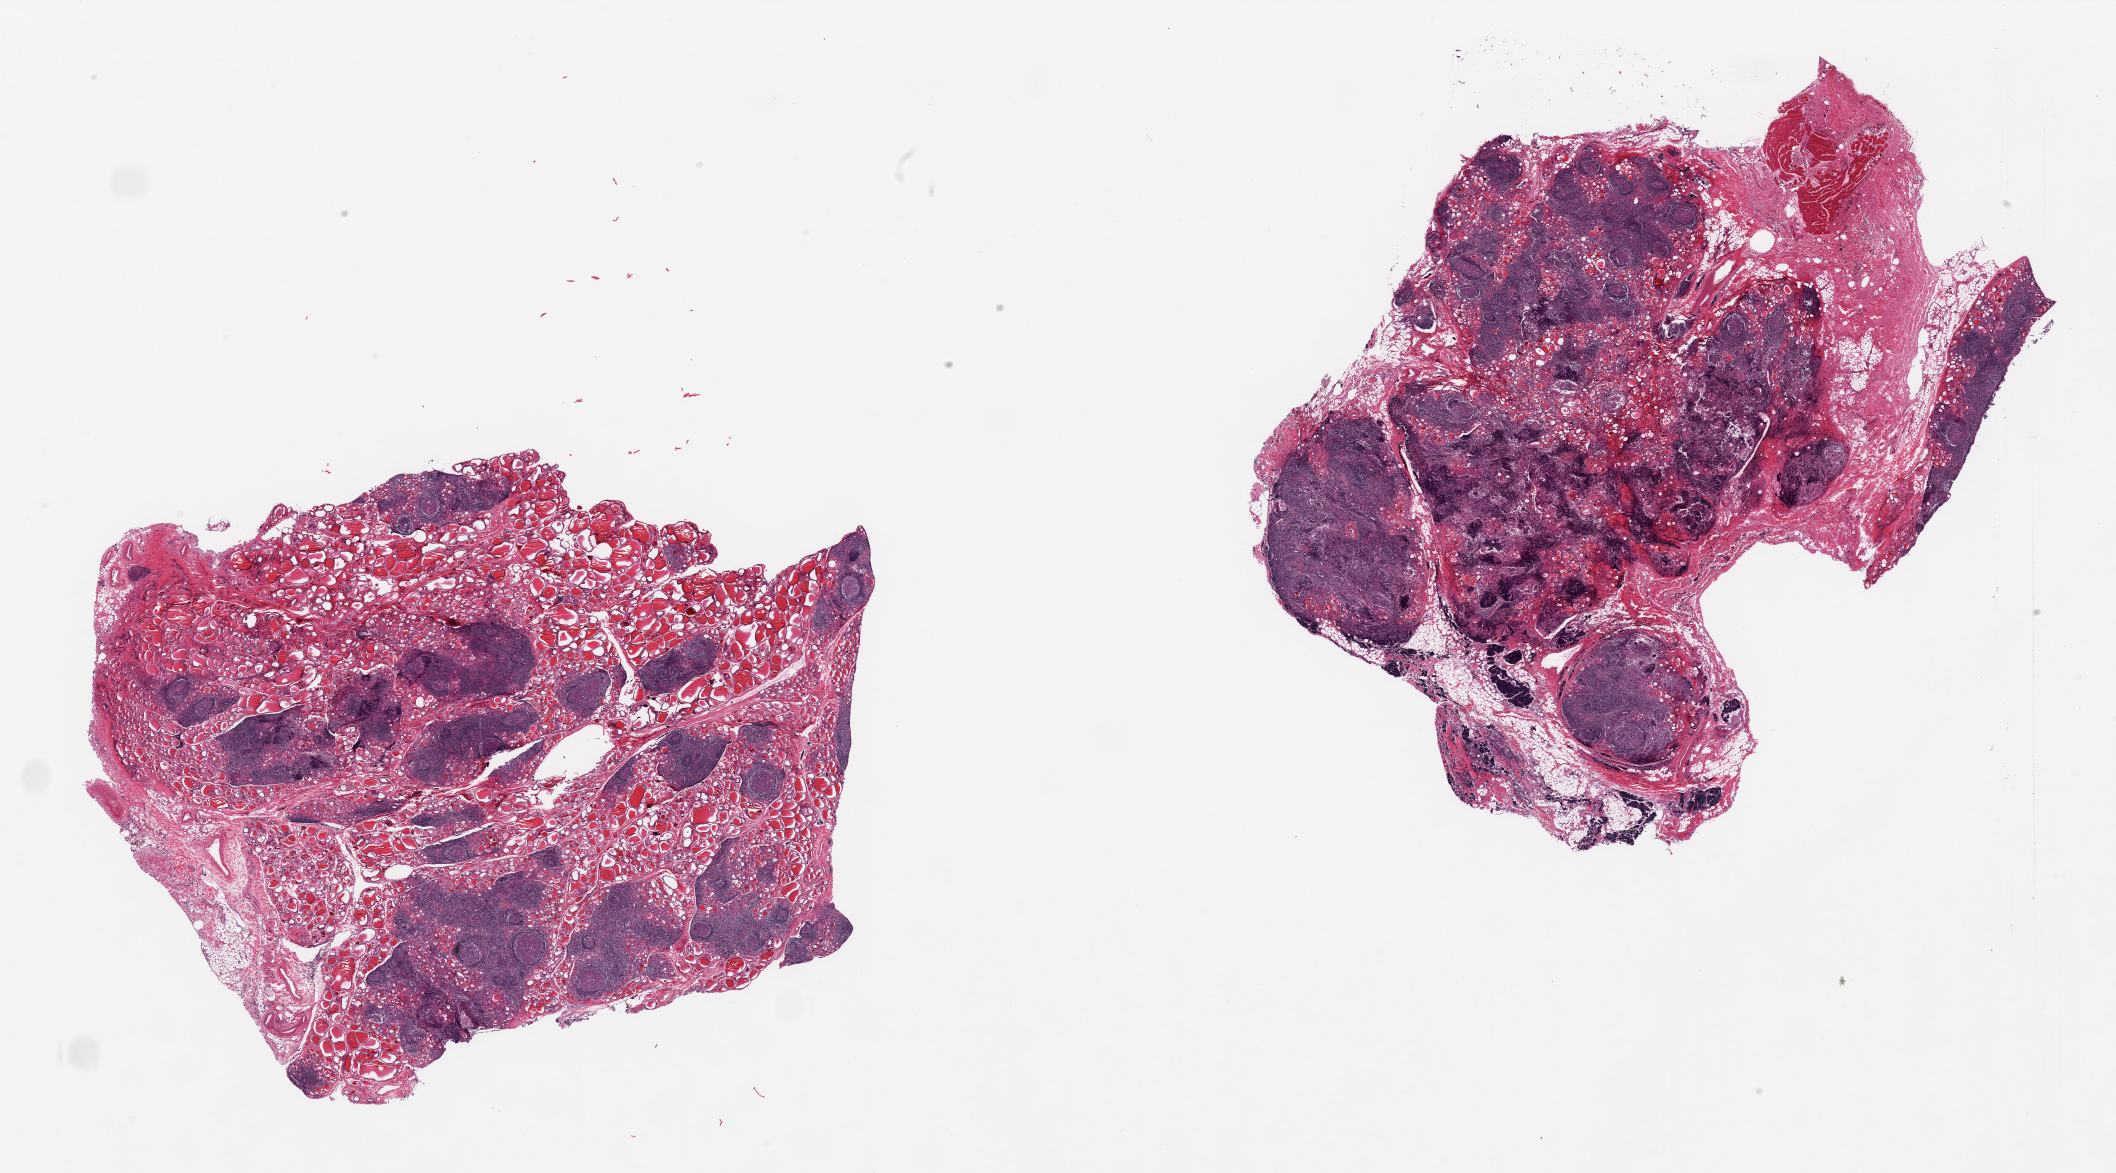
Haematoxylin and eosin whole-slide image, brightfield — shown as a low-resolution overview of the whole scanned area (about 33.5 x 18.6 mm, slide scanned at 20x), PAXgene-fixed, paraffin-embedded tissue, target tissue: thyroid, tissue donor sample. Donor: male.
• reviewer comment on this tissue sample: 2 pieces, prominent Hashimoto thyroiditis with regressive changes; rep lymphoid aggregates